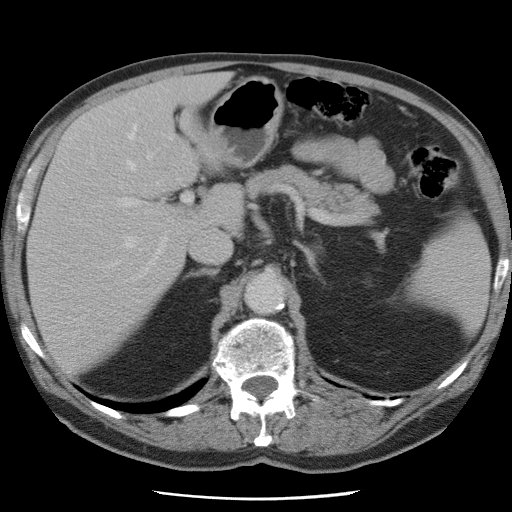
Contrast-enhanced abdominal CT, one axial slice; position 47 of 78 along the scan axis; intravenous contrast given; soft-tissue window (W 400 / L 40 HU); 512 × 512 image matrix, field of view 337 × 337 mm. Male patient, age 75 years. Case-level facts recorded for this patient, not image findings: diagnosis: colorectal cancer liver metastases, imaged before liver resection; multiple liver metastases: yes; largest metastasis: 2.4 cm; disease in both lobes: yes.
Annotated regions visible in this slice (expert manual segmentation):
- hepatic veins: box from (x=73, y=125) to (x=159, y=269) px
- liver: (x=29, y=75)–(x=244, y=373)
- planned liver remnant (the part of the liver to remain after resection): (x=28, y=122)–(x=194, y=373)
- portal vein (with intrahepatic branches): (x=118, y=135)–(x=192, y=277)